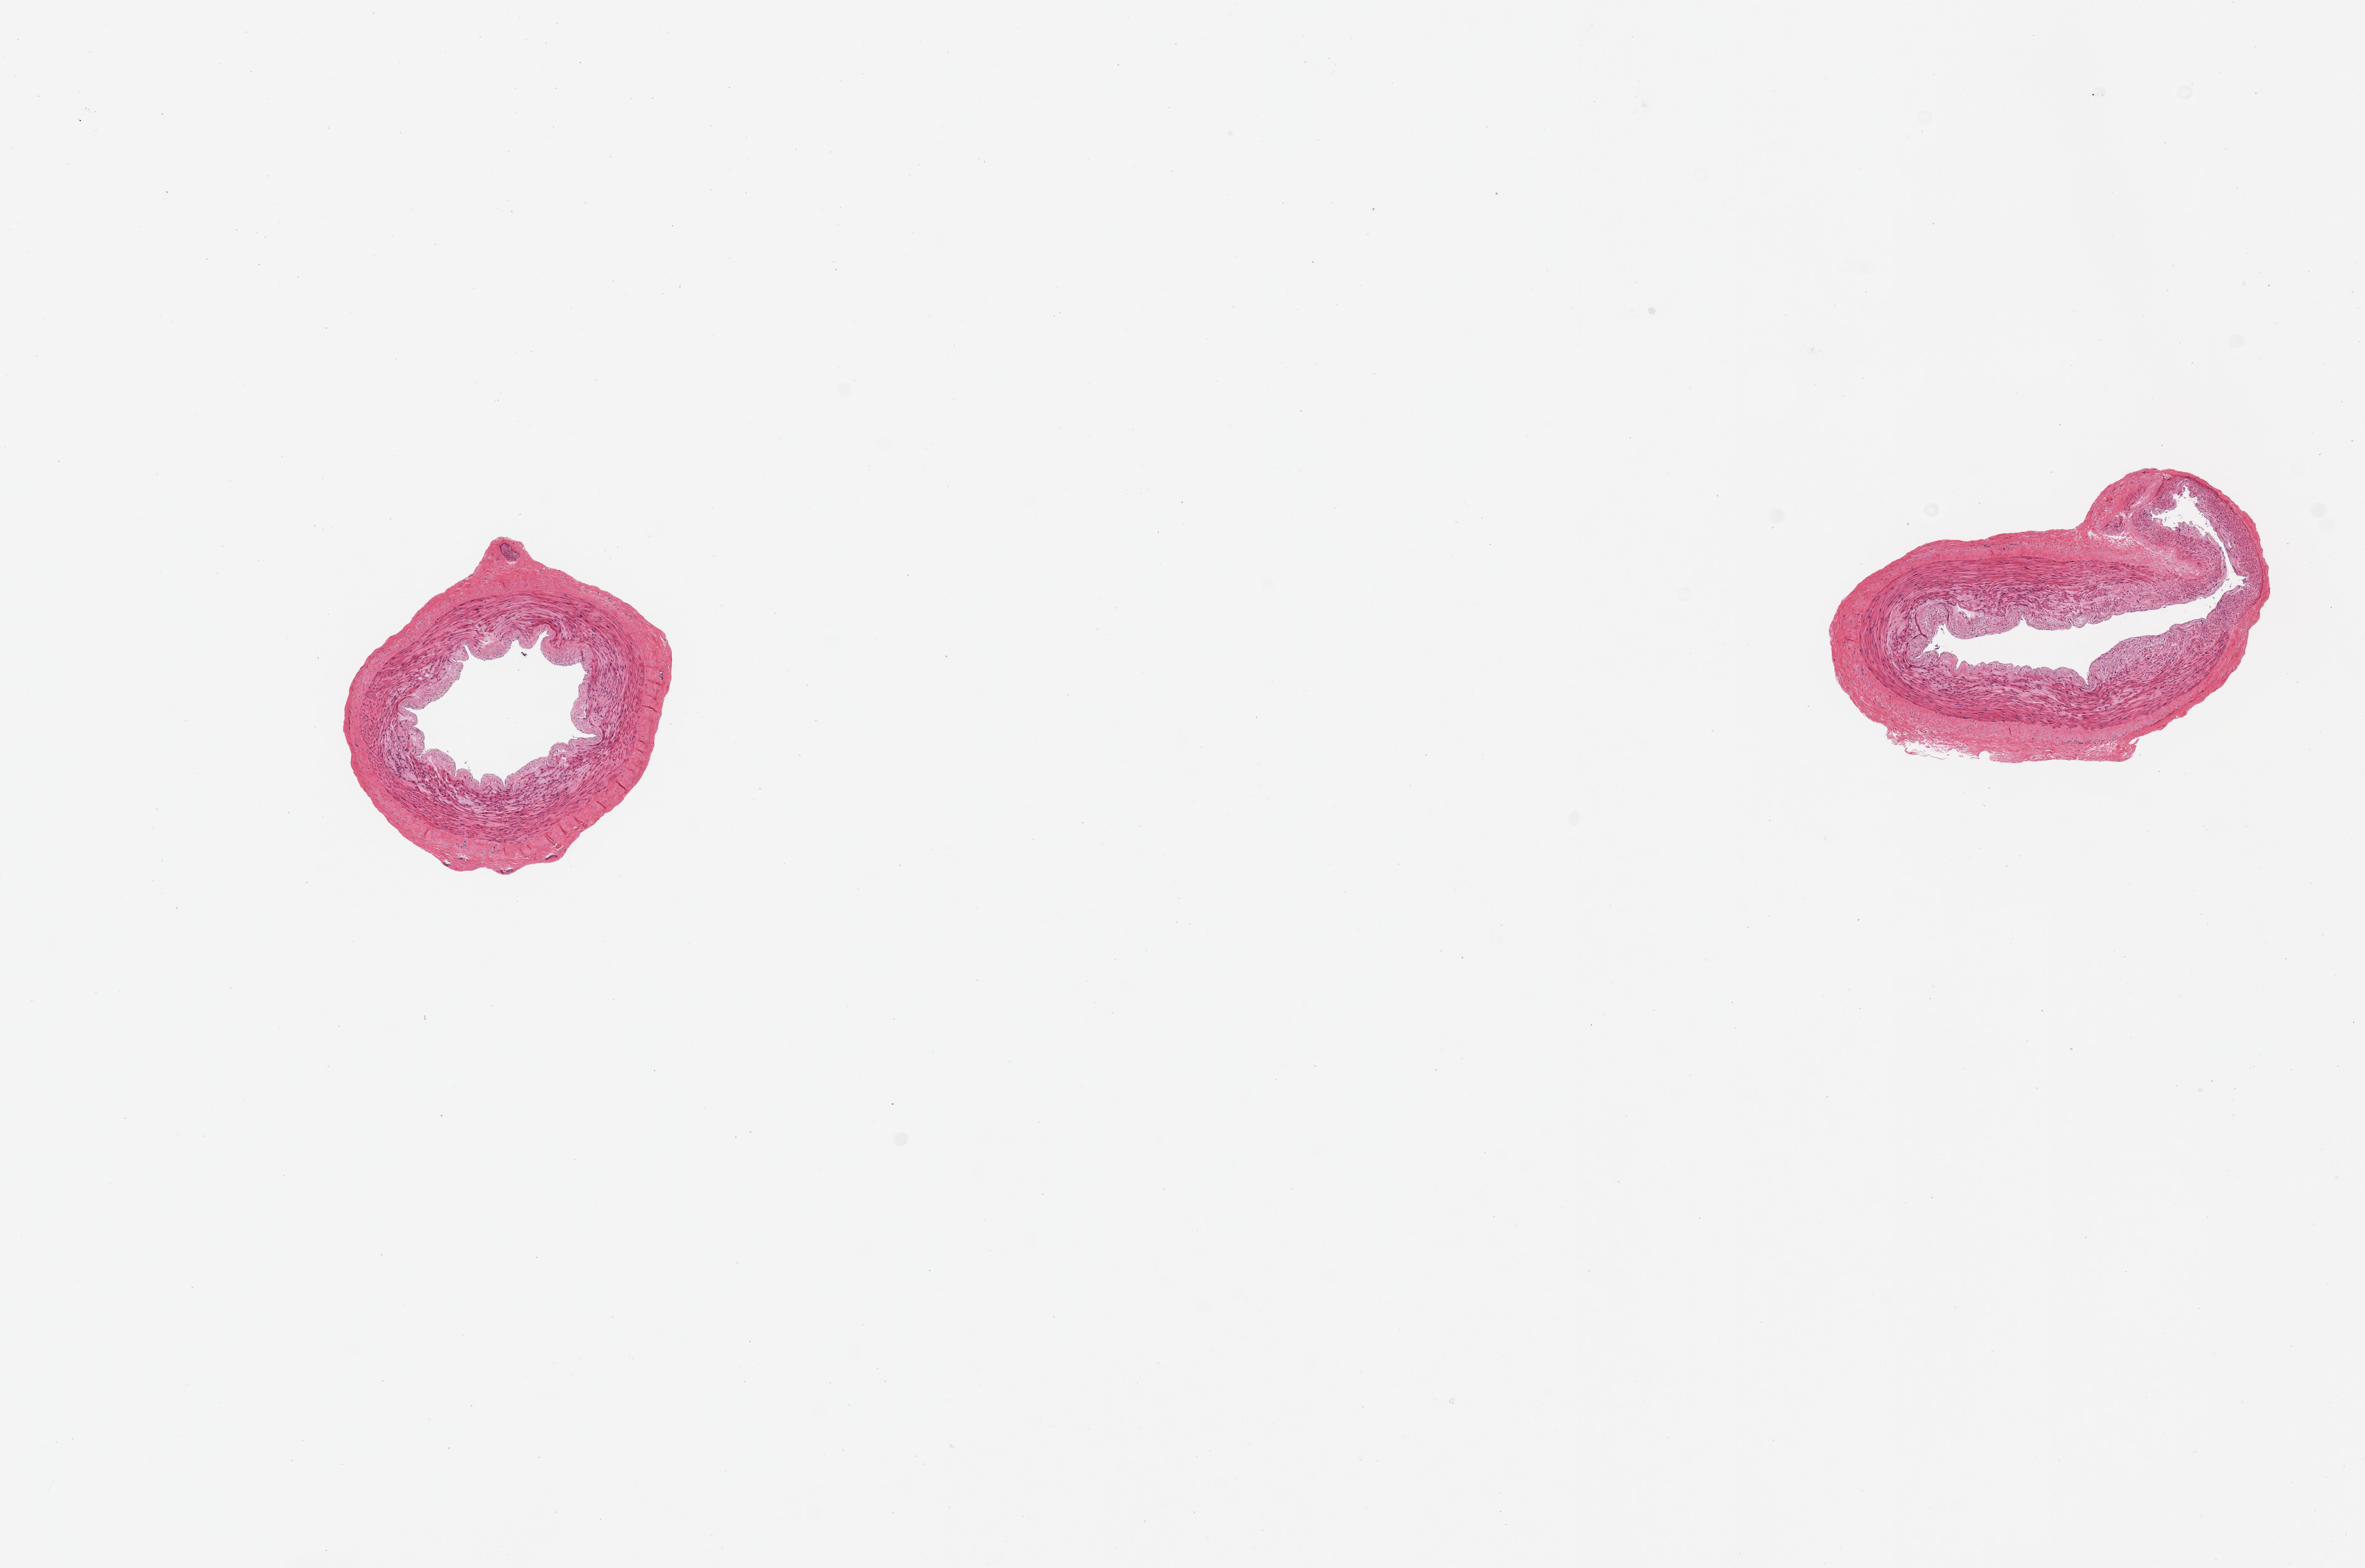
Digitized hematoxylin and eosin (H&E)-stained section — shown as a low-resolution overview of the whole scanned area (about 14.8 x 9.8 mm); PAXgene-fixed paraffin-embedded (PFPE) section; target tissue: tibial artery; donor tissue sample. Donor sex: male.
- review note (as recorded): 2 pieces; no plaques